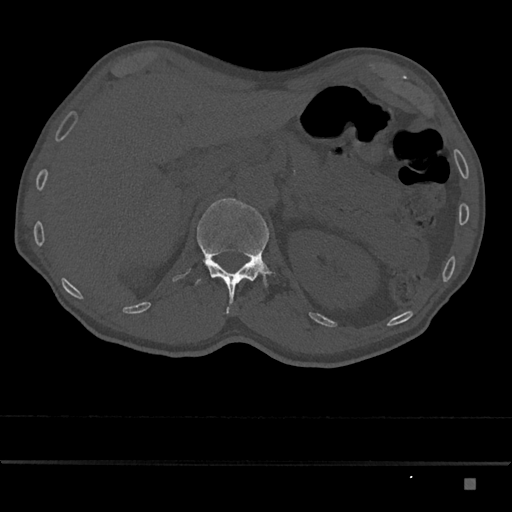
CT including the spine, one axial slice. Slice 545 of 797 in the series (ordered by position). Reconstruction kernel Br40s/3. 120 kVp. Bone window (W 1800 / L 400 HU). 0.5 mm slice thickness. 512 × 512 image matrix. Patient: male, 72 years. Case-level facts recorded for this patient, not image findings: primary cancer: prostate.
Structures marked on this image (semi-automatic segmentation, software-assisted and operator-edited):
- L1 vertebra: bounding box <196,198,286,314> (left, top, right, bottom; pixels)